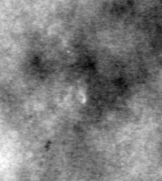
Cropped region of a digitized screen-film mammogram centred on a radiologist-marked abnormality, right breast, CC view, BI-RADS breast density category 3 (scale 1–4).
Marked abnormality: calcifications, morphology pleomorphic, distribution clustered; BI-RADS assessment category 4; subtlety rating 3 on a 1 (subtle) to 5 (obvious) scale; pathology result (as recorded, not read from the image): benign.